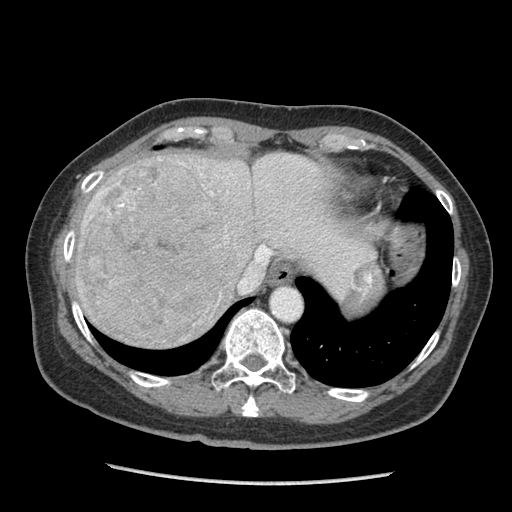
Contrast-enhanced abdominal CT (liver protocol), one axial slice; position 75 of 105 along the scan axis; reconstruction kernel STANDARD; 140 kVp; soft-tissue window (W 400 / L 40 HU); 2.5 mm slice thickness; 512 × 512 image matrix, field of view 340 × 340 mm. From the clinical record (not read from this slice): diagnosis: hepatocellular carcinoma (patient treated with transarterial chemoembolisation; whether this scan precedes or follows treatment is not stated here); TNM stage (as recorded): Stage-I; Child-Pugh class: A; tumour nodularity: uninodular; tumour size: 11.1 cm.
Structures marked on this image (semi-automatically segmented with operator editing):
- abdominal aorta: bounding box <272,288,301,319> (left, top, right, bottom; pixels)
- liver parenchyma outside the tumour (the mass and vessels are separate outlines, so this box may not span the whole liver): <72,150,374,330>
- mass: <75,155,230,347>